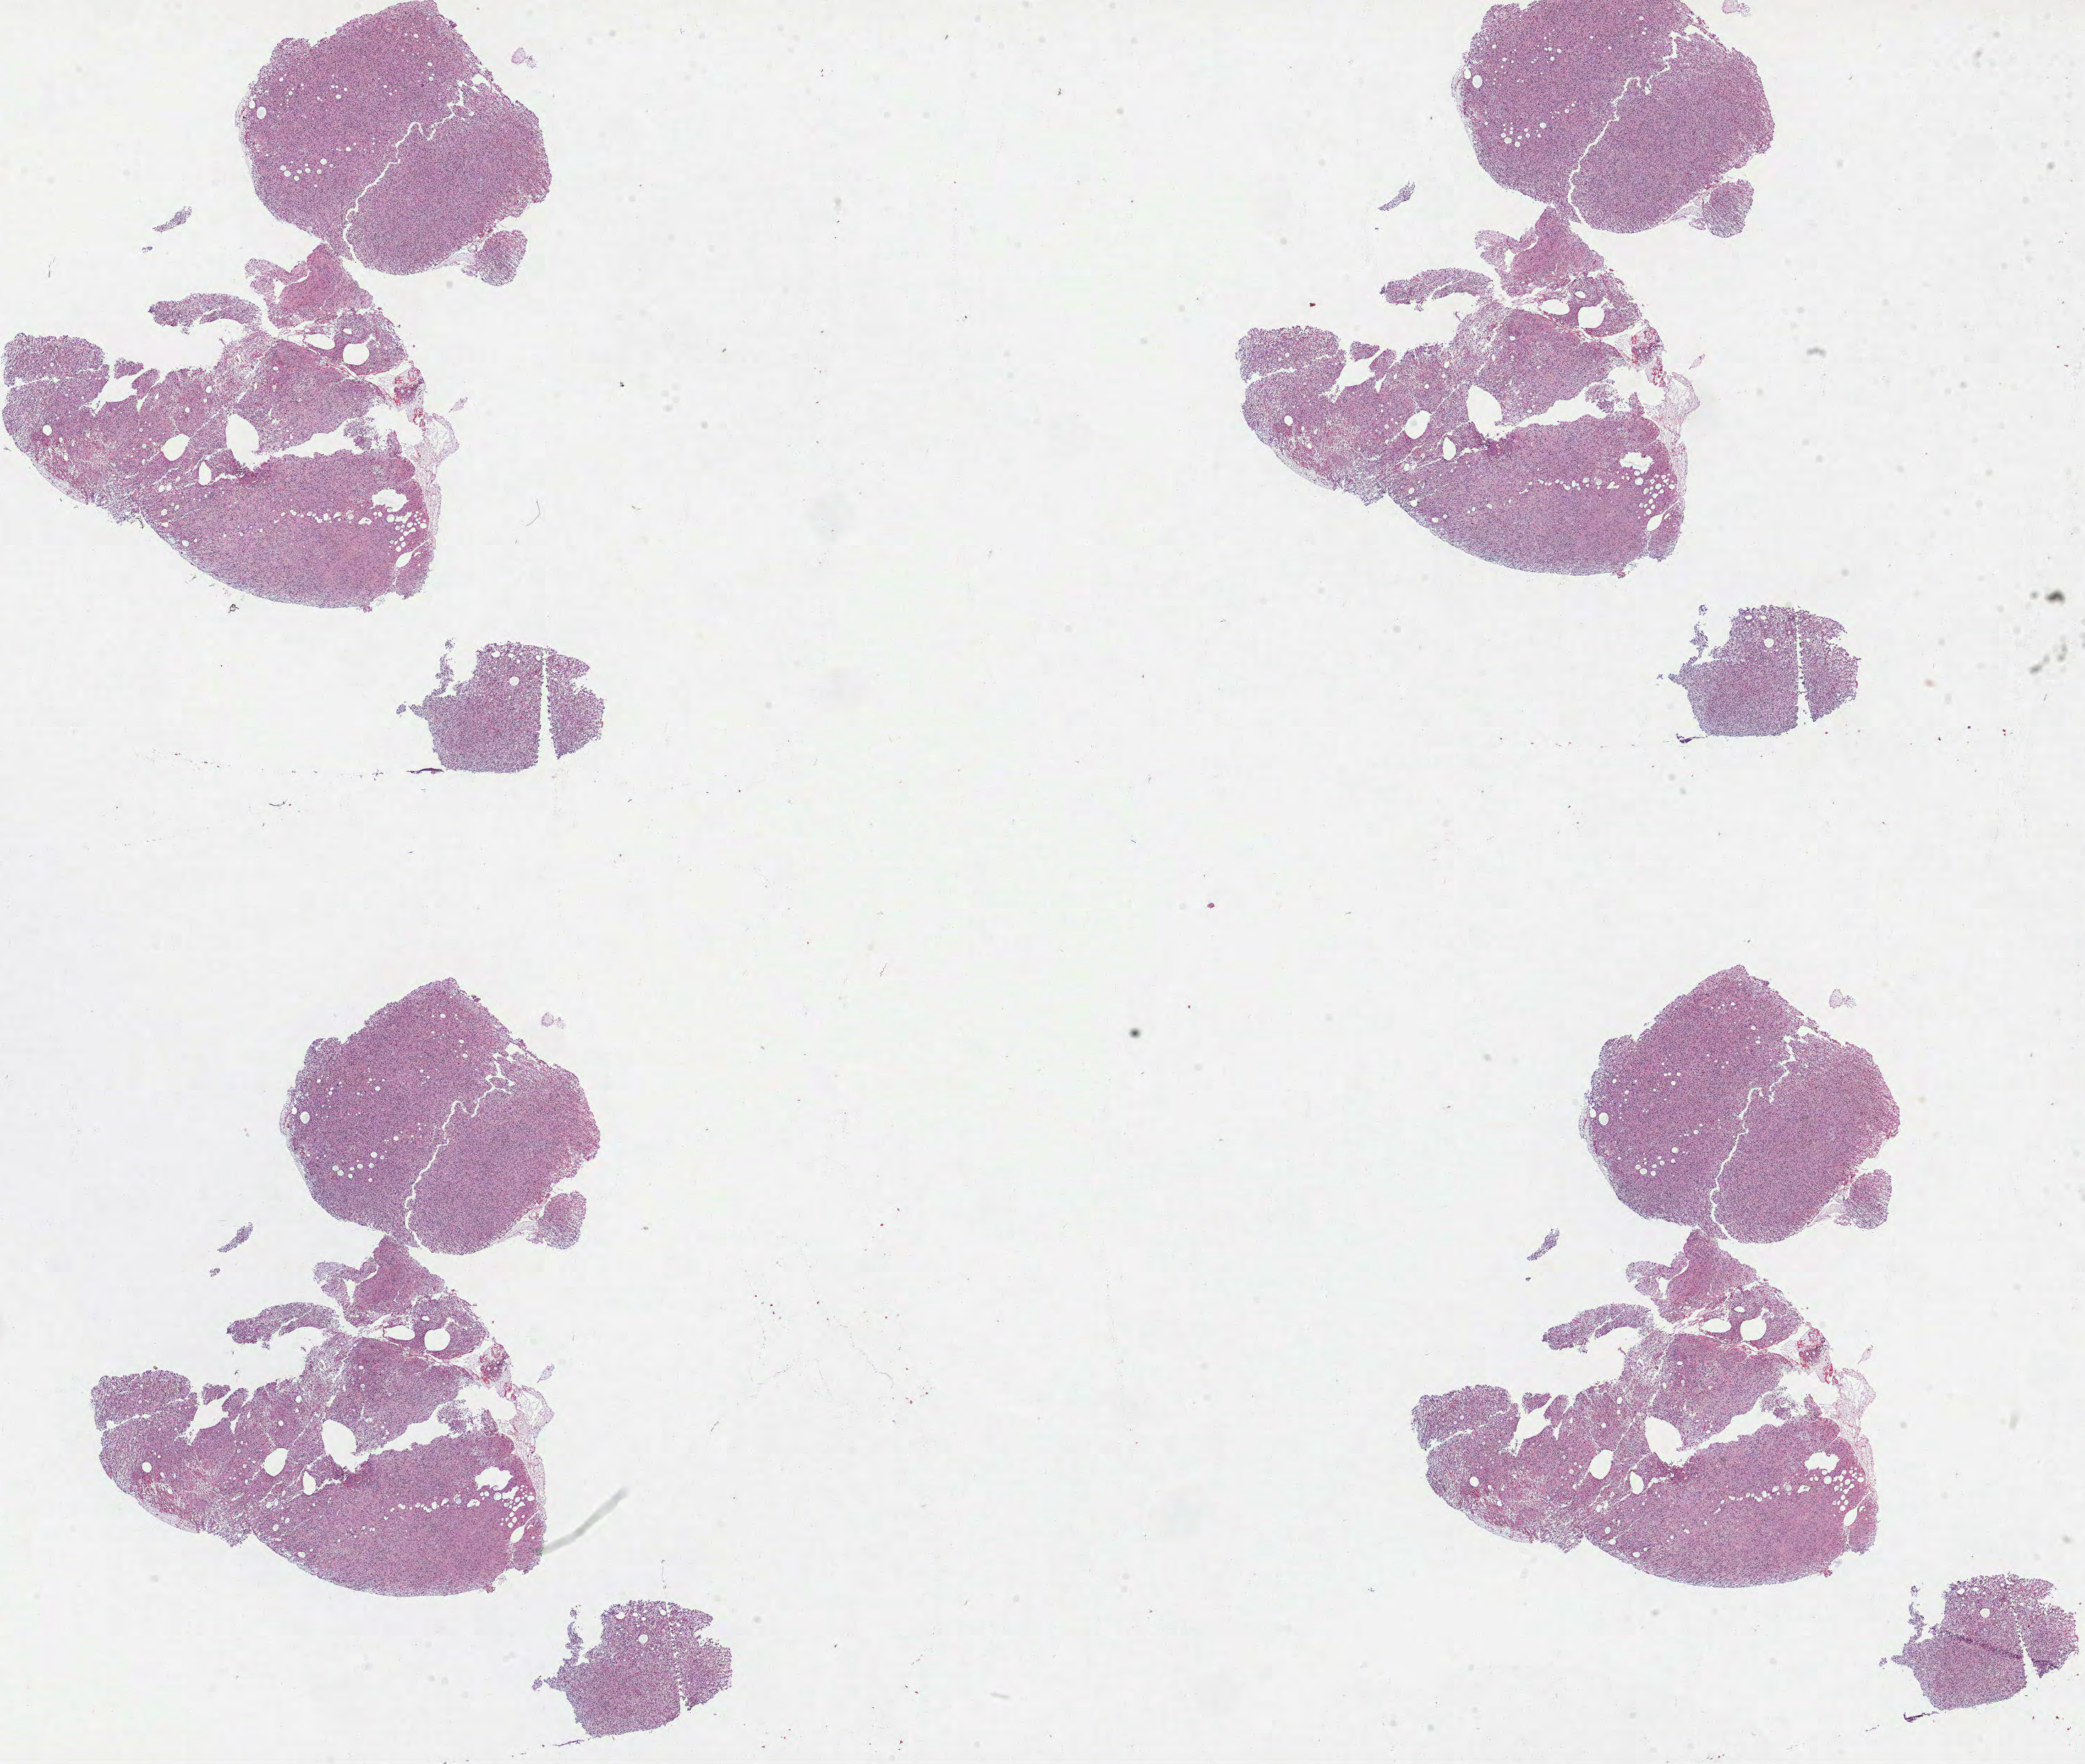
Digitized Hematoxylin and eosin (H&E) stained tissue section (whole slide), a low-resolution overview of the entire scanned area, about 23.7 x 20.0 mm (acquisition: 40x scan), FFPE section, primary tumour sample from the brain. Male patient; age at initial diagnosis 52 years. Histologic grade: G3 (poorly differentiated).
Histologic diagnosis: Astrocytoma, anaplastic.